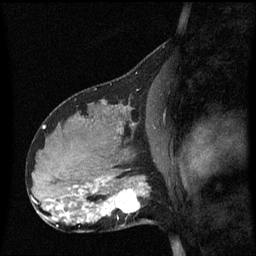
Breast MRI (dynamic contrast-enhanced), one sagittal slice; slice 32 of 60 in the series (ordered by position); dynamic contrast-enhanced series, image 2 of 3 at this slice position (ordered by acquisition); 1.5 T; TE 4.2 ms, TR 8.4 ms; 2.1 mm slice thickness; 256 × 256 image matrix. Female patient, age 31 years. From the clinical record (not read from this slice): setting: breast cancer imaged before/during neoadjuvant chemotherapy; receptor status: HR-positive, HER2-negative.
Annotated regions visible in this slice (semi-automatic segmentation, software-assisted and operator-edited):
- analysis volume of interest (the breast-tissue region the enhancement analysis was run in; not a lesion): bounding box [x1, y1, x2, y2] px = [98, 175, 154, 228]
- tumour enhancement mask (voxels above the 70 % enhancement threshold inside the analysis volume of interest): [102, 182, 146, 216]